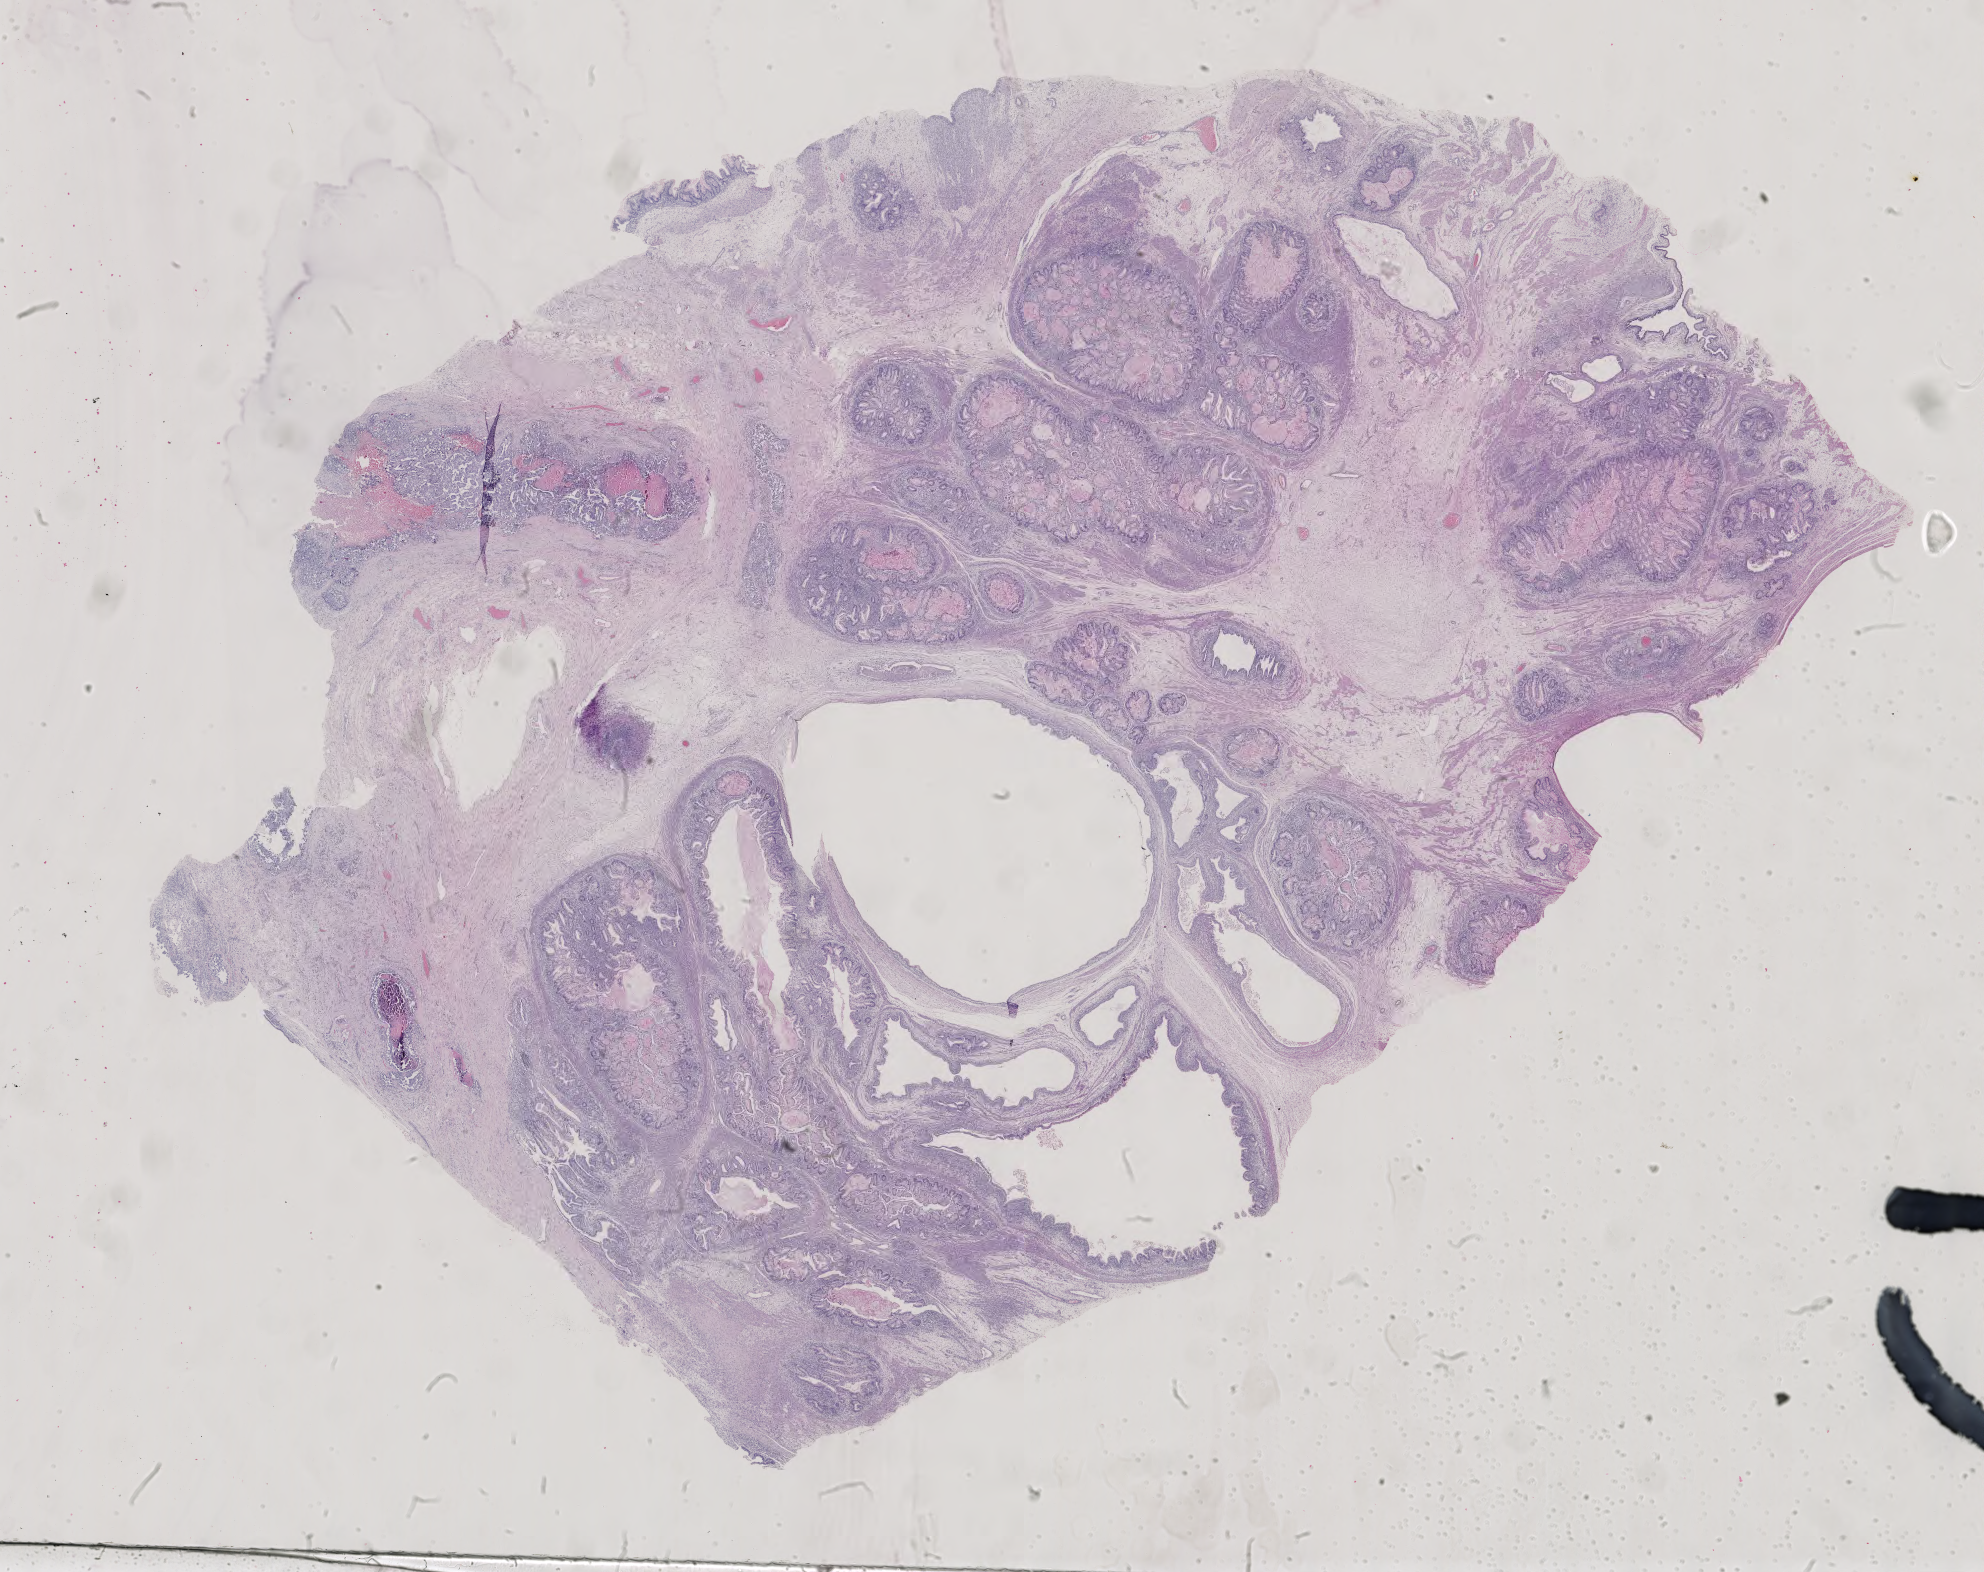
Whole-slide histology image, H&E — a low-resolution overview of the entire scanned area, about 28.9 x 22.9 mm. Formalin-fixed paraffin-embedded (FFPE) diagnostic section. Primary tumour sample from the testis. Male, age 36 years at initial diagnosis.
Laterality: left. AJCC pathologic stage: IS (6th edition). Diagnosis: Teratoma, benign.